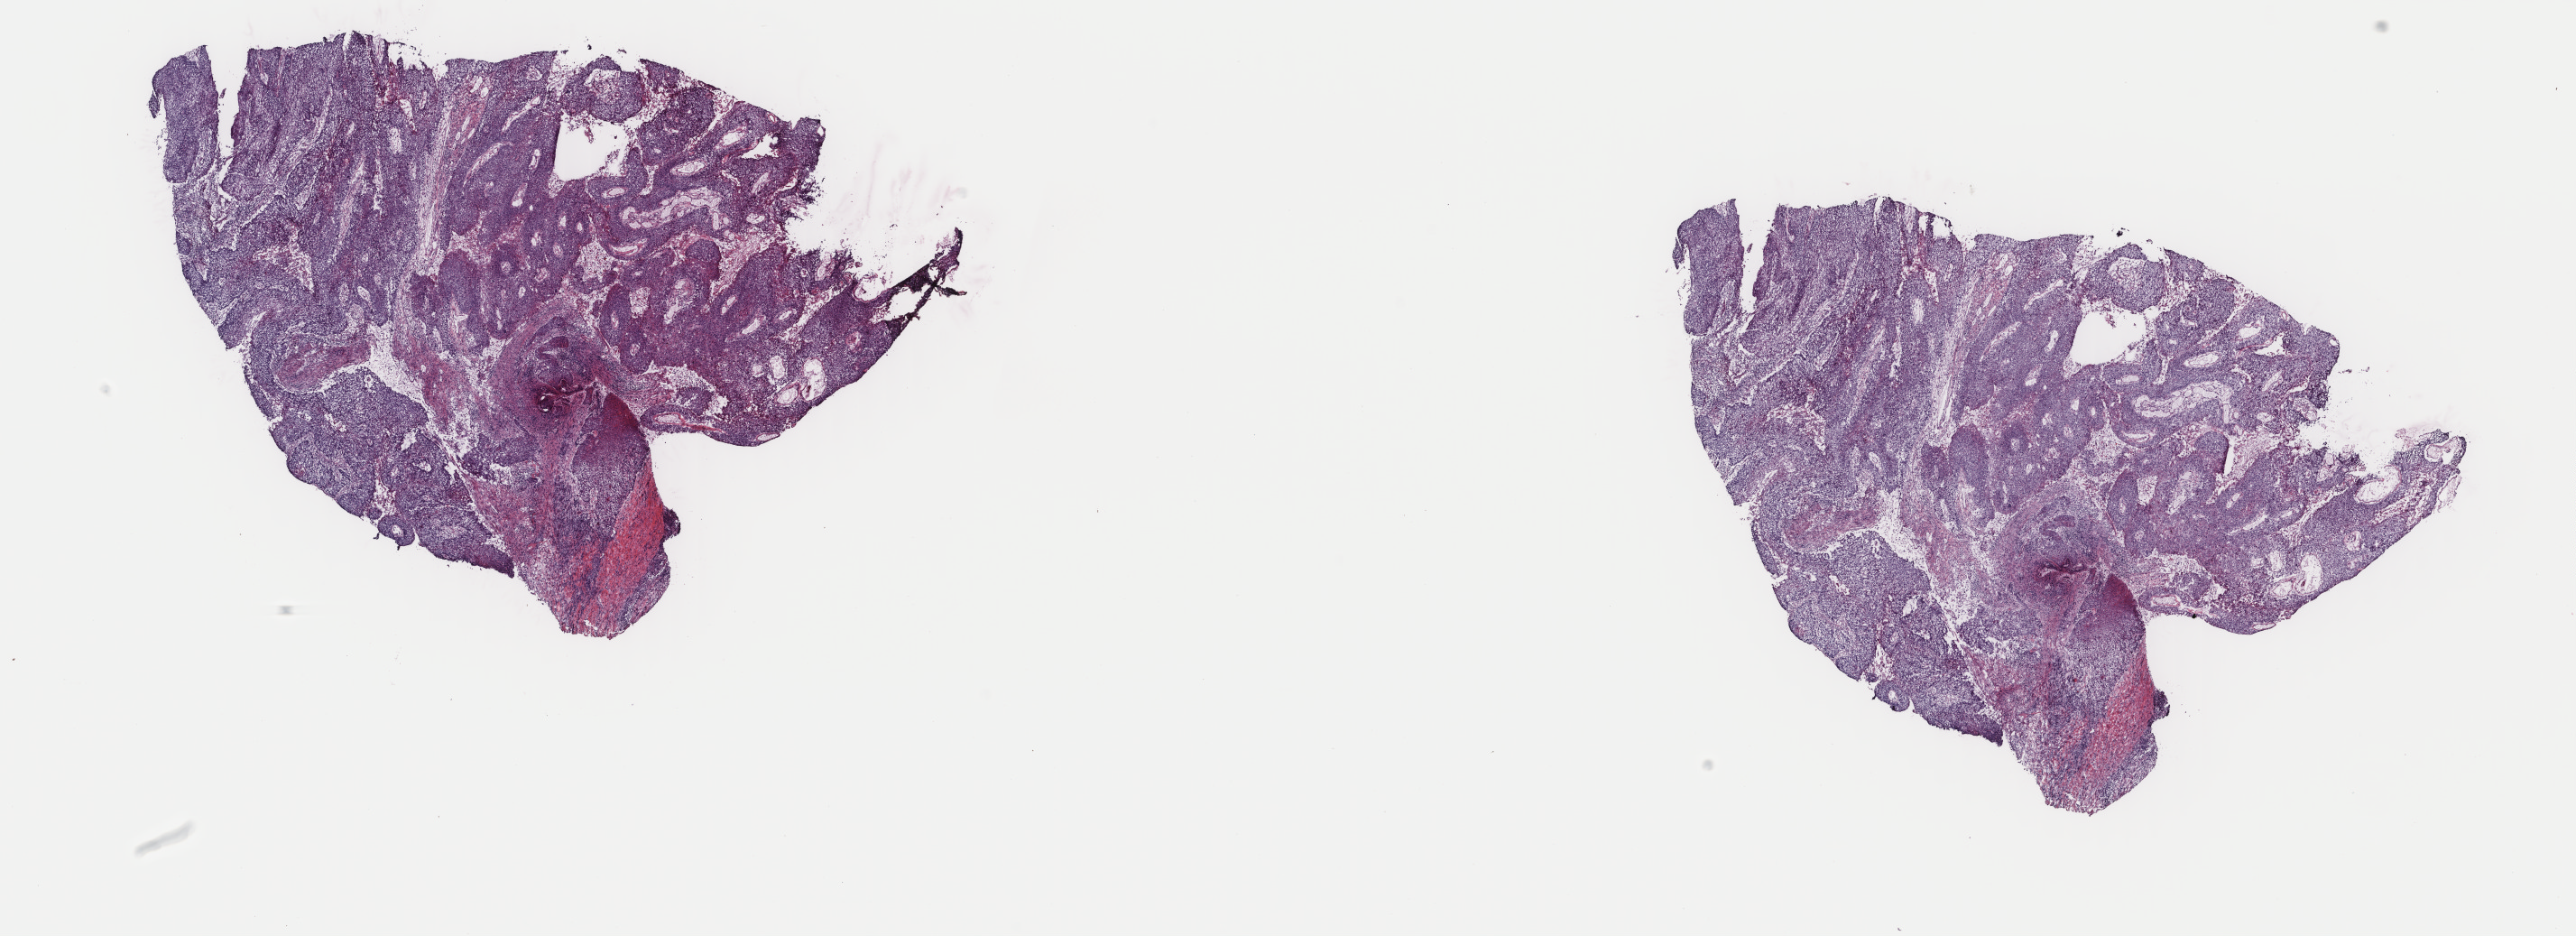
Whole-slide histology image, H&E, low-resolution overview of the scanned area, about 22.7 x 8.2 mm; frozen section from the top of the tissue portion; sample: primary tumour, lung. Patient: male, age at initial diagnosis 52 years. Slide review estimates, as recorded: tumour cells 98%, tumour nuclei 75%, normal cells 0%, stromal cells 0%, necrosis 2%. Infiltration values recorded for this section: lymphocyte infiltration 0%, monocyte infiltration 0%, neutrophil infiltration 0%.
* AJCC pathologic stage: IB
* TNM: T2a N0 M0
* histologic diagnosis: Basaloid squamous cell carcinoma (lower lobe, lung)
* laterality: right